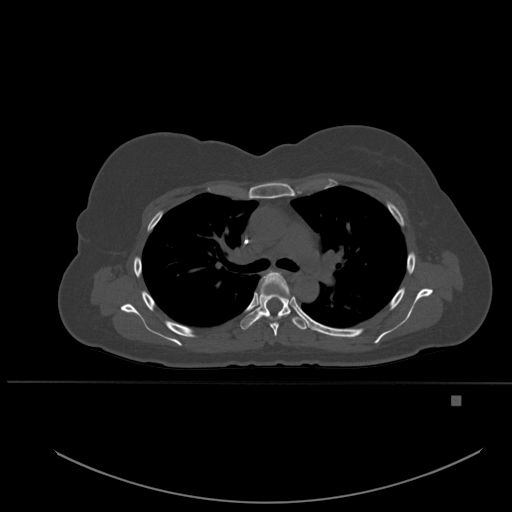
CT including the spine, one axial slice. Position 371 of 651 along the scan axis. Bone window (W 1800 / L 400 HU). 512 × 512 image matrix, field of view 443 × 443 mm. Patient: female, 49 years. Case-level facts recorded for this patient, not image findings: primary cancer: breast.
Outlined on this slice (semi-automatically segmented with operator editing):
- T4 vertebra: bounding box [x1, y1, x2, y2] px = [261, 270, 290, 337]
- T5 vertebra: [240, 290, 307, 330]